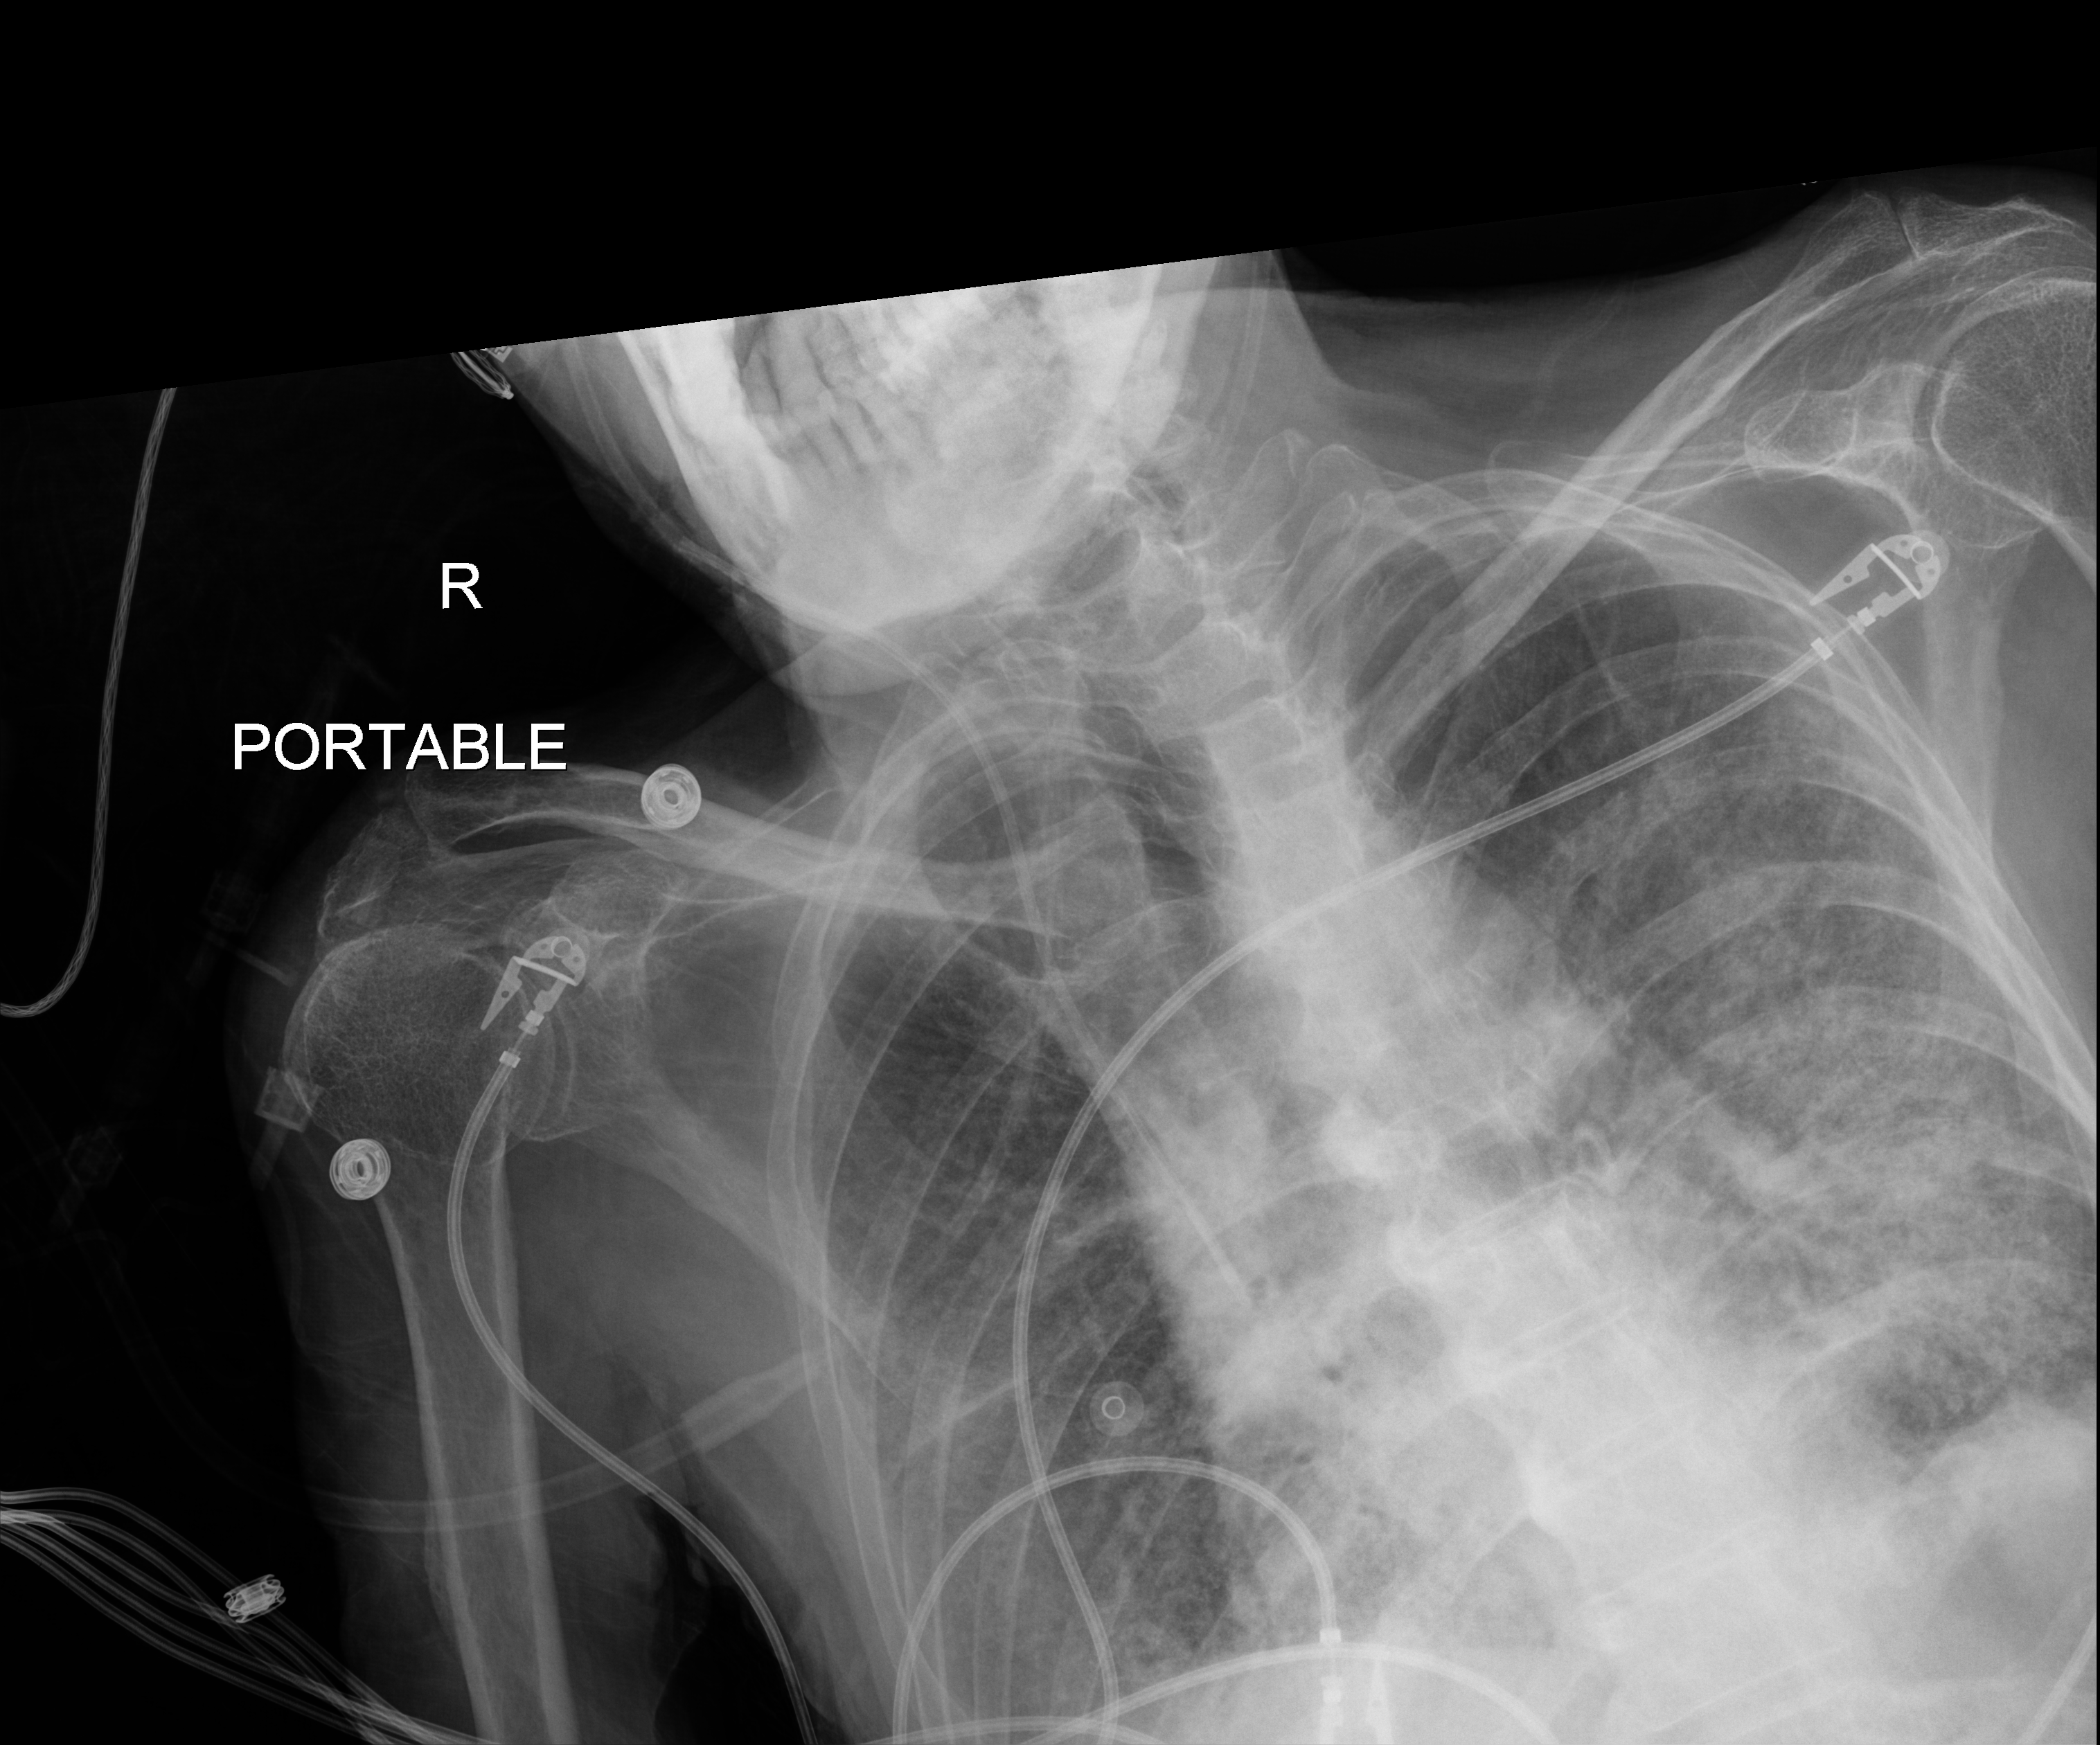
Chest X-ray (portable); anteroposterior (AP) projection. Male patient hospitalised with COVID-19, age 60–74 years.
Admission-level facts for this patient (not findings on this image; timing relative to this image not recorded):
- smoking status (admission record): current